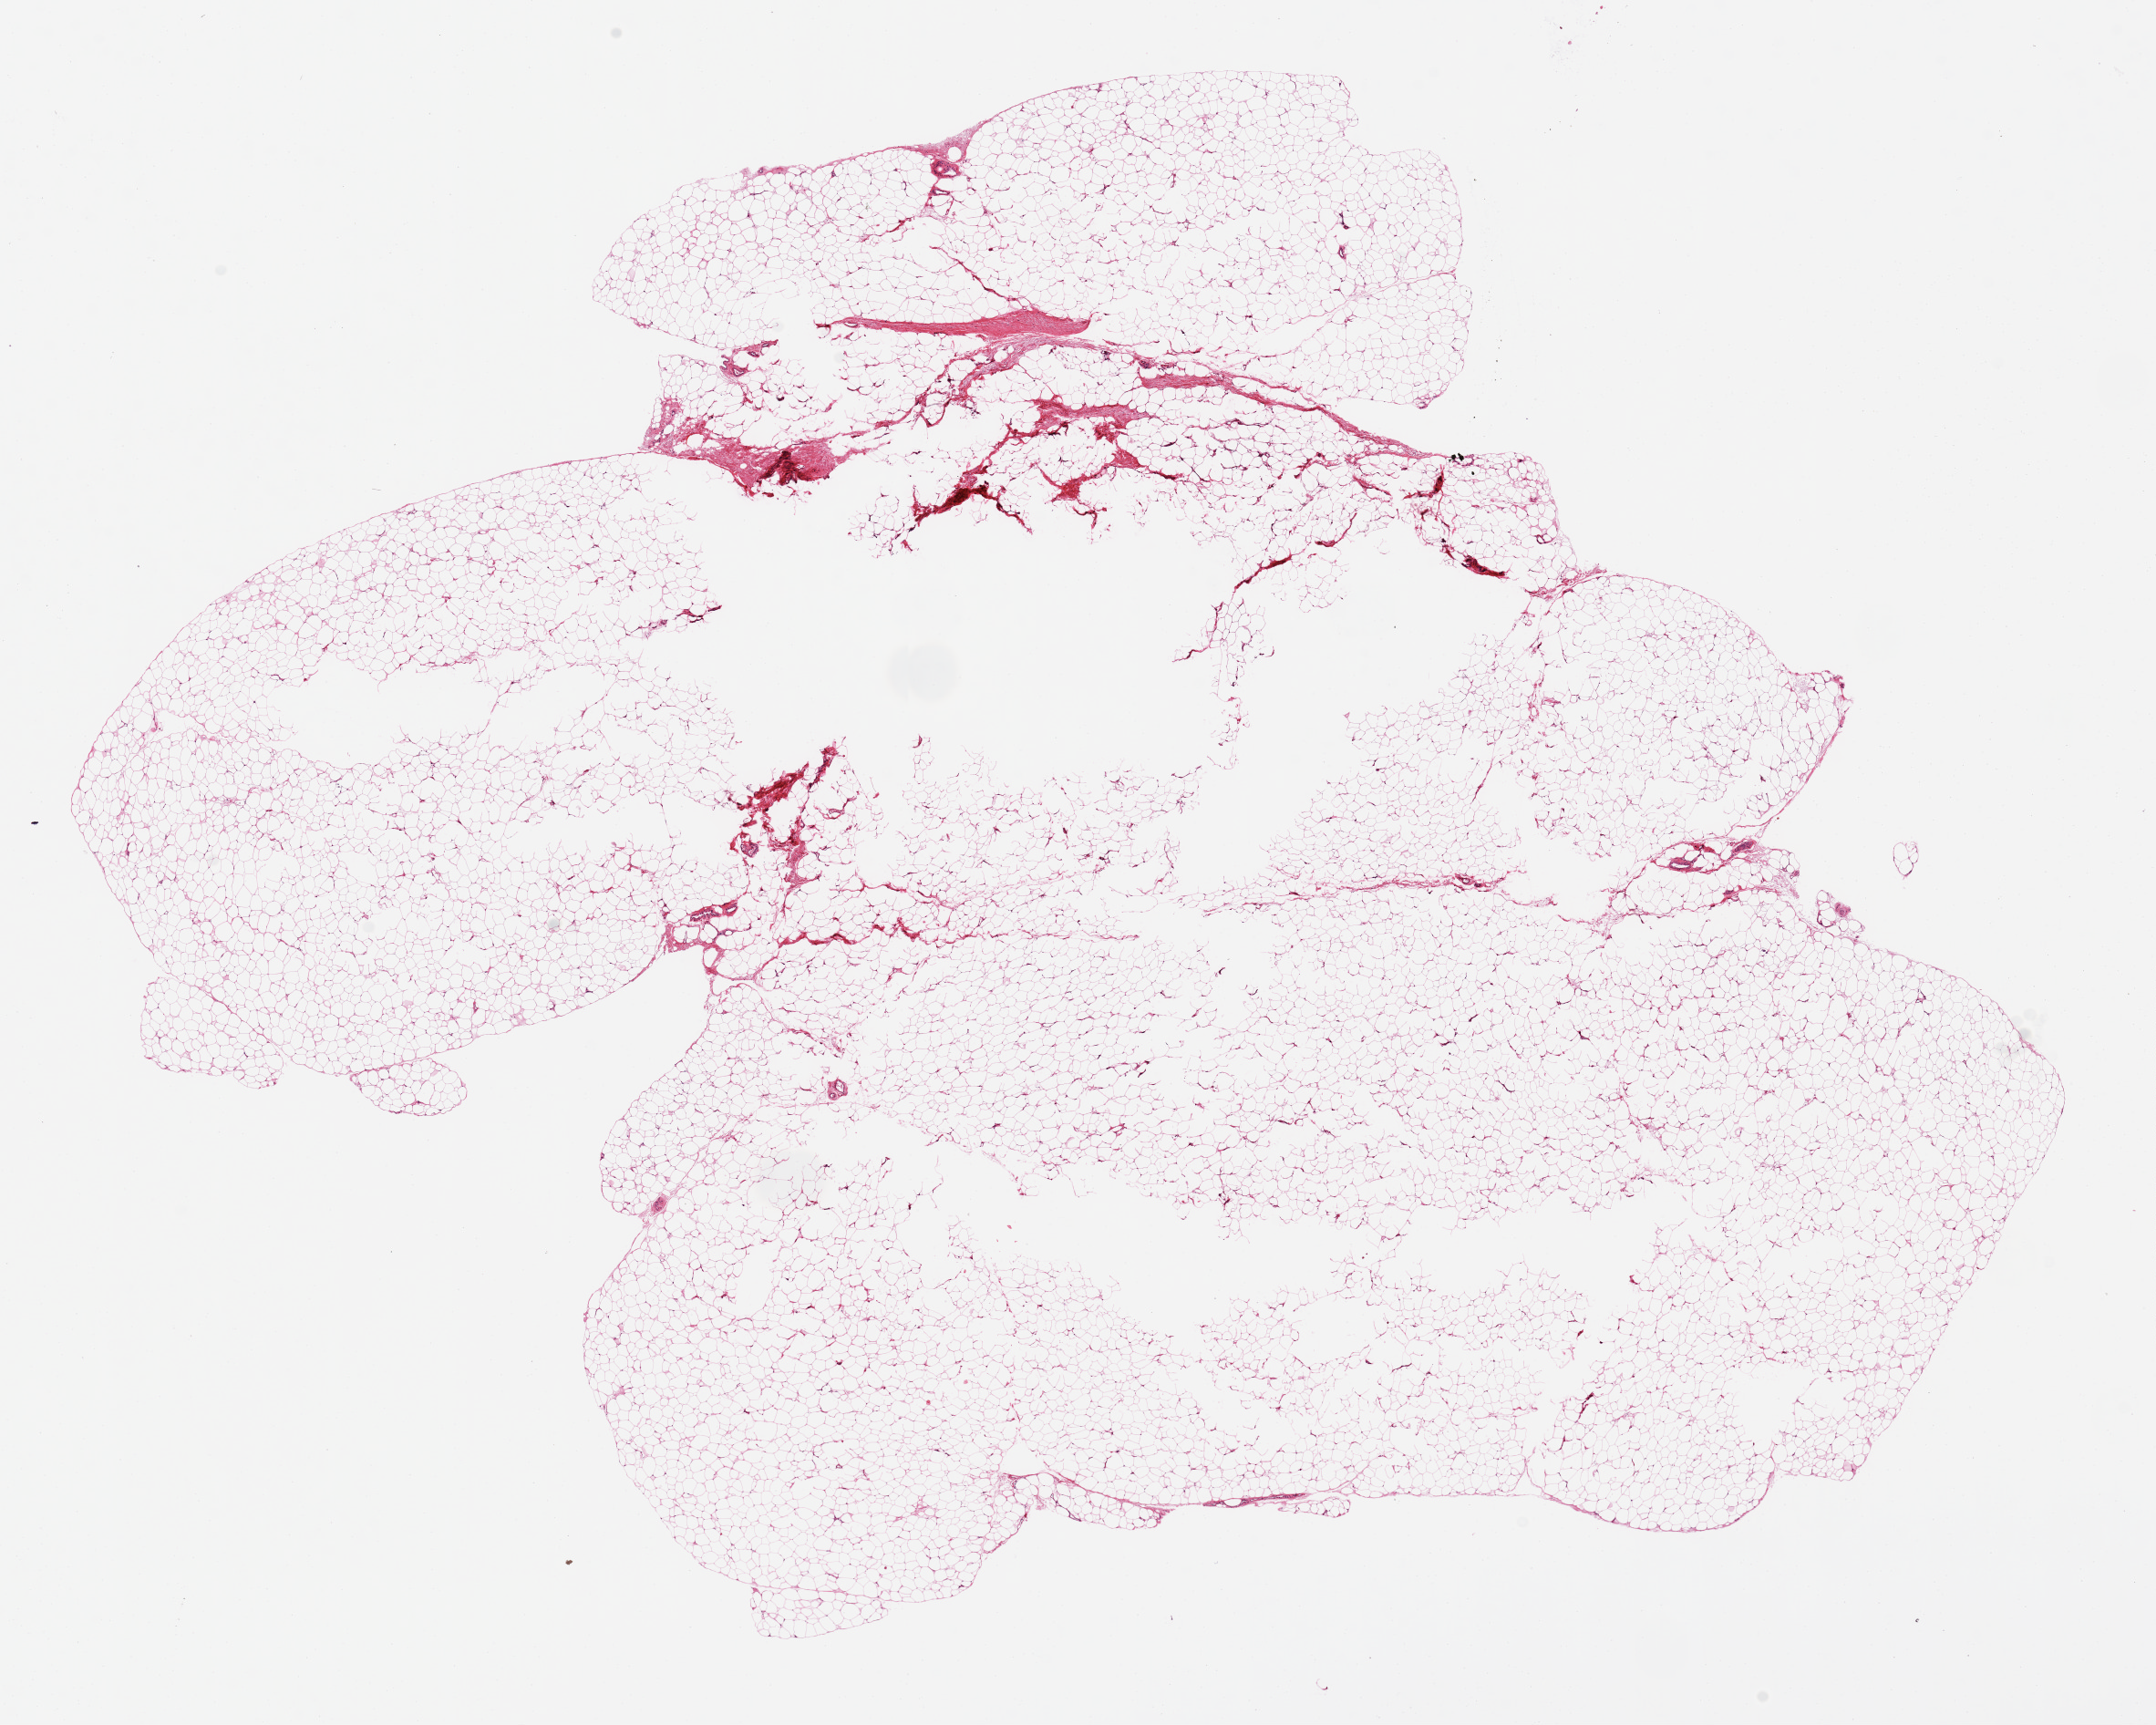
Whole-slide image, H&E stain, whole scanned area (about 18.7 x 15.0 mm) shown as a low-resolution overview; PAXgene-fixed paraffin-embedded (PFPE) section; section of adipose tissue (target tissue); tissue donor sample. Donor: female.
Pathologist's review note for this sample: Large 16x12.8 aliquot. Most appears empty with central unfixed spaces.